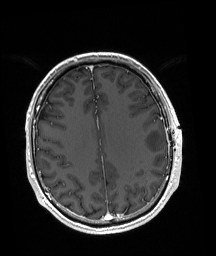
Brain MRI from a brain-tumour surgery series, one axial slice. Slice 68 of 192 in the series (ordered by position). T1-weighted post-contrast. 1 mm slice thickness. 216 × 256 image matrix, field of view 211 × 250 mm. From the clinical record (not read from this slice): histopathology: Astrocytoma; WHO grade: 3; IDH mutation: yes; tumour location: Left Posterior Frontal.
Outlined on this slice (expert manual segmentation):
- tumour: bounding box [x1, y1, x2, y2] px = [143, 129, 165, 152]